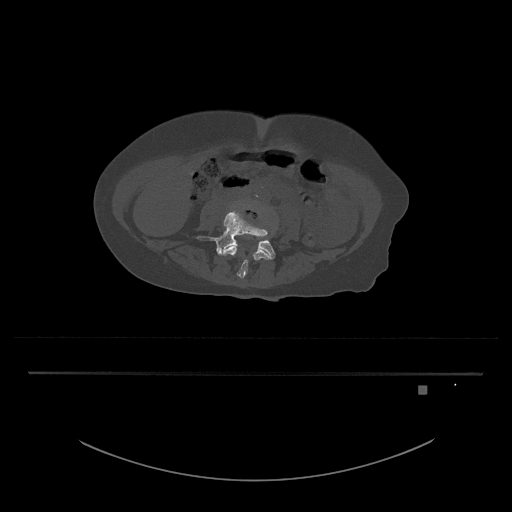
CT including the spine, one axial slice. Slice 330 of 797 in the series (ordered by position). Bone window (W 1800 / L 400 HU). 512 × 512 image matrix, field of view 500 × 500 mm. Female patient, age 57 years. From the clinical record (not read from this slice): primary cancer: cervical.
Annotated regions visible in this slice (semi-automatically segmented with operator editing):
- L4 vertebra: box from (x=222, y=208) to (x=272, y=279) px